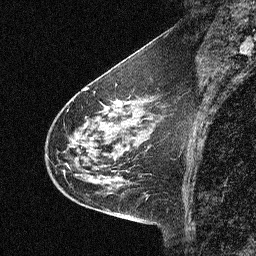
Breast MRI (dynamic contrast-enhanced), one sagittal slice. Dynamic contrast-enhanced study with each time point stored as its own series, time point 2 of 3 at this slice position (early post-contrast, ordered by acquisition time). 1.5 T. TE 4.5 ms, TR 11 ms. 2.06 mm slice thickness. 256 × 256 image matrix, field of view 200 × 200 mm. Patient: female, 46 years. From the clinical record (not read from this slice): setting: breast cancer imaged before/during neoadjuvant chemotherapy; receptor status: HER2-positive.
Annotated regions visible in this slice (semi-automatically segmented with operator editing):
- analysis volume of interest (the breast-tissue region the enhancement analysis was run in; not a lesion): bounding box <42,80,150,180> (left, top, right, bottom; pixels)
- tumour enhancement mask (voxels above the 90 % enhancement threshold inside the analysis volume of interest): <68,91,136,161>